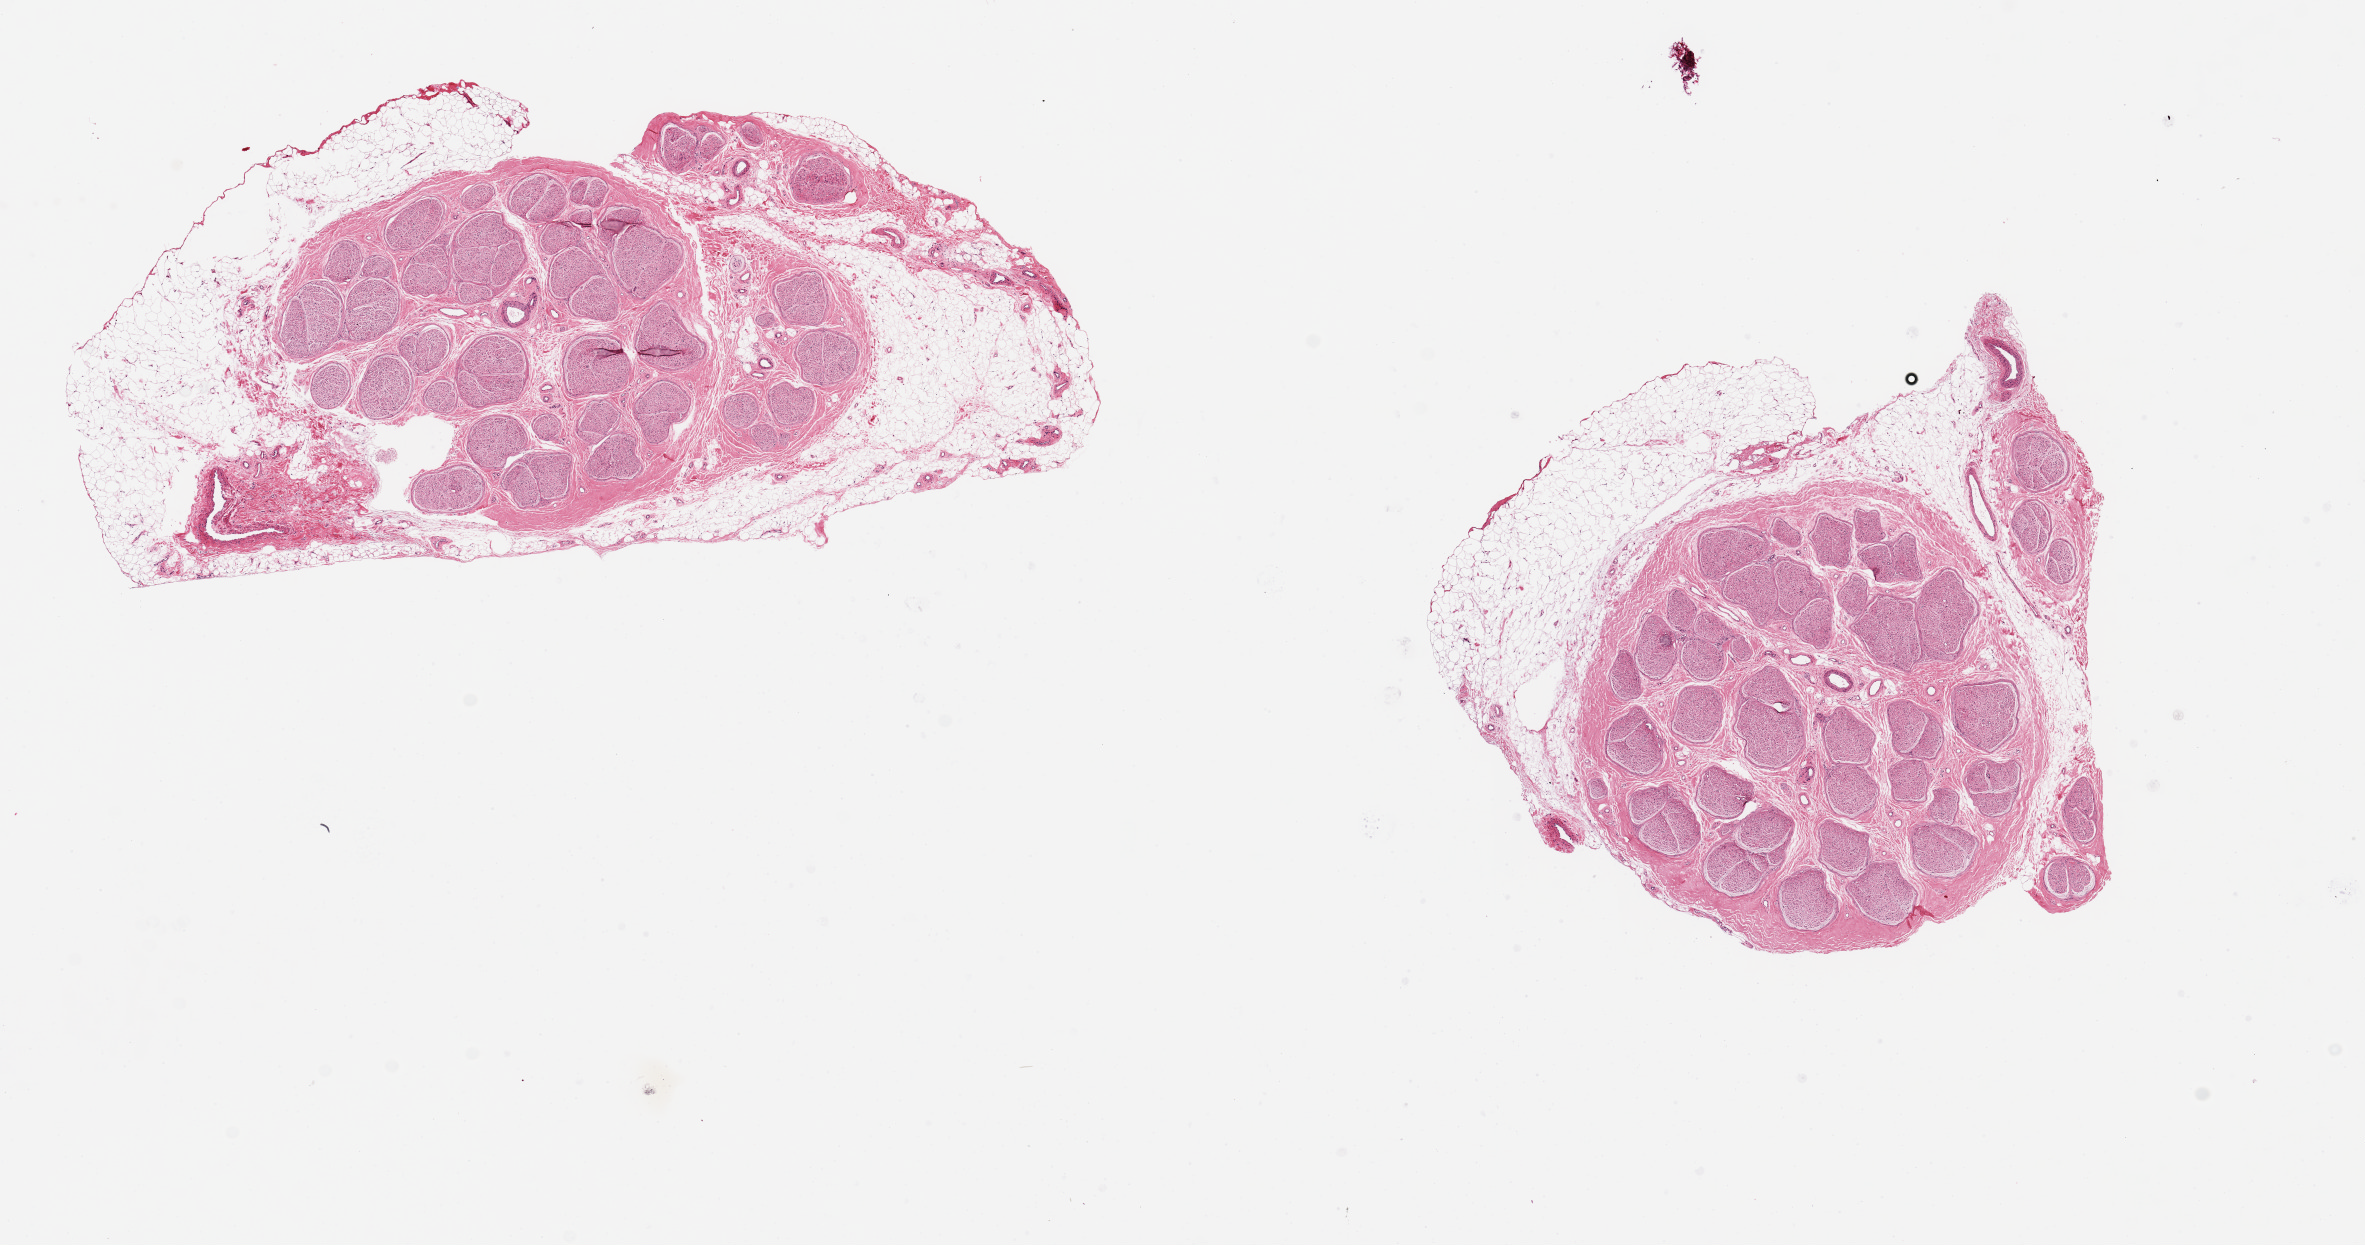
Hematoxylin and eosin (H&E) whole-slide image, low-resolution overview of the scanned area, about 18.7 x 9.8 mm. PAXgene-fixed, paraffin-embedded tissue. Target tissue: tibial nerve. Tissue donor sample.
Pathologist's review note for this sample: 2 pieces ~4mm d. Adherent fat up to ~1.5mm thick on both.